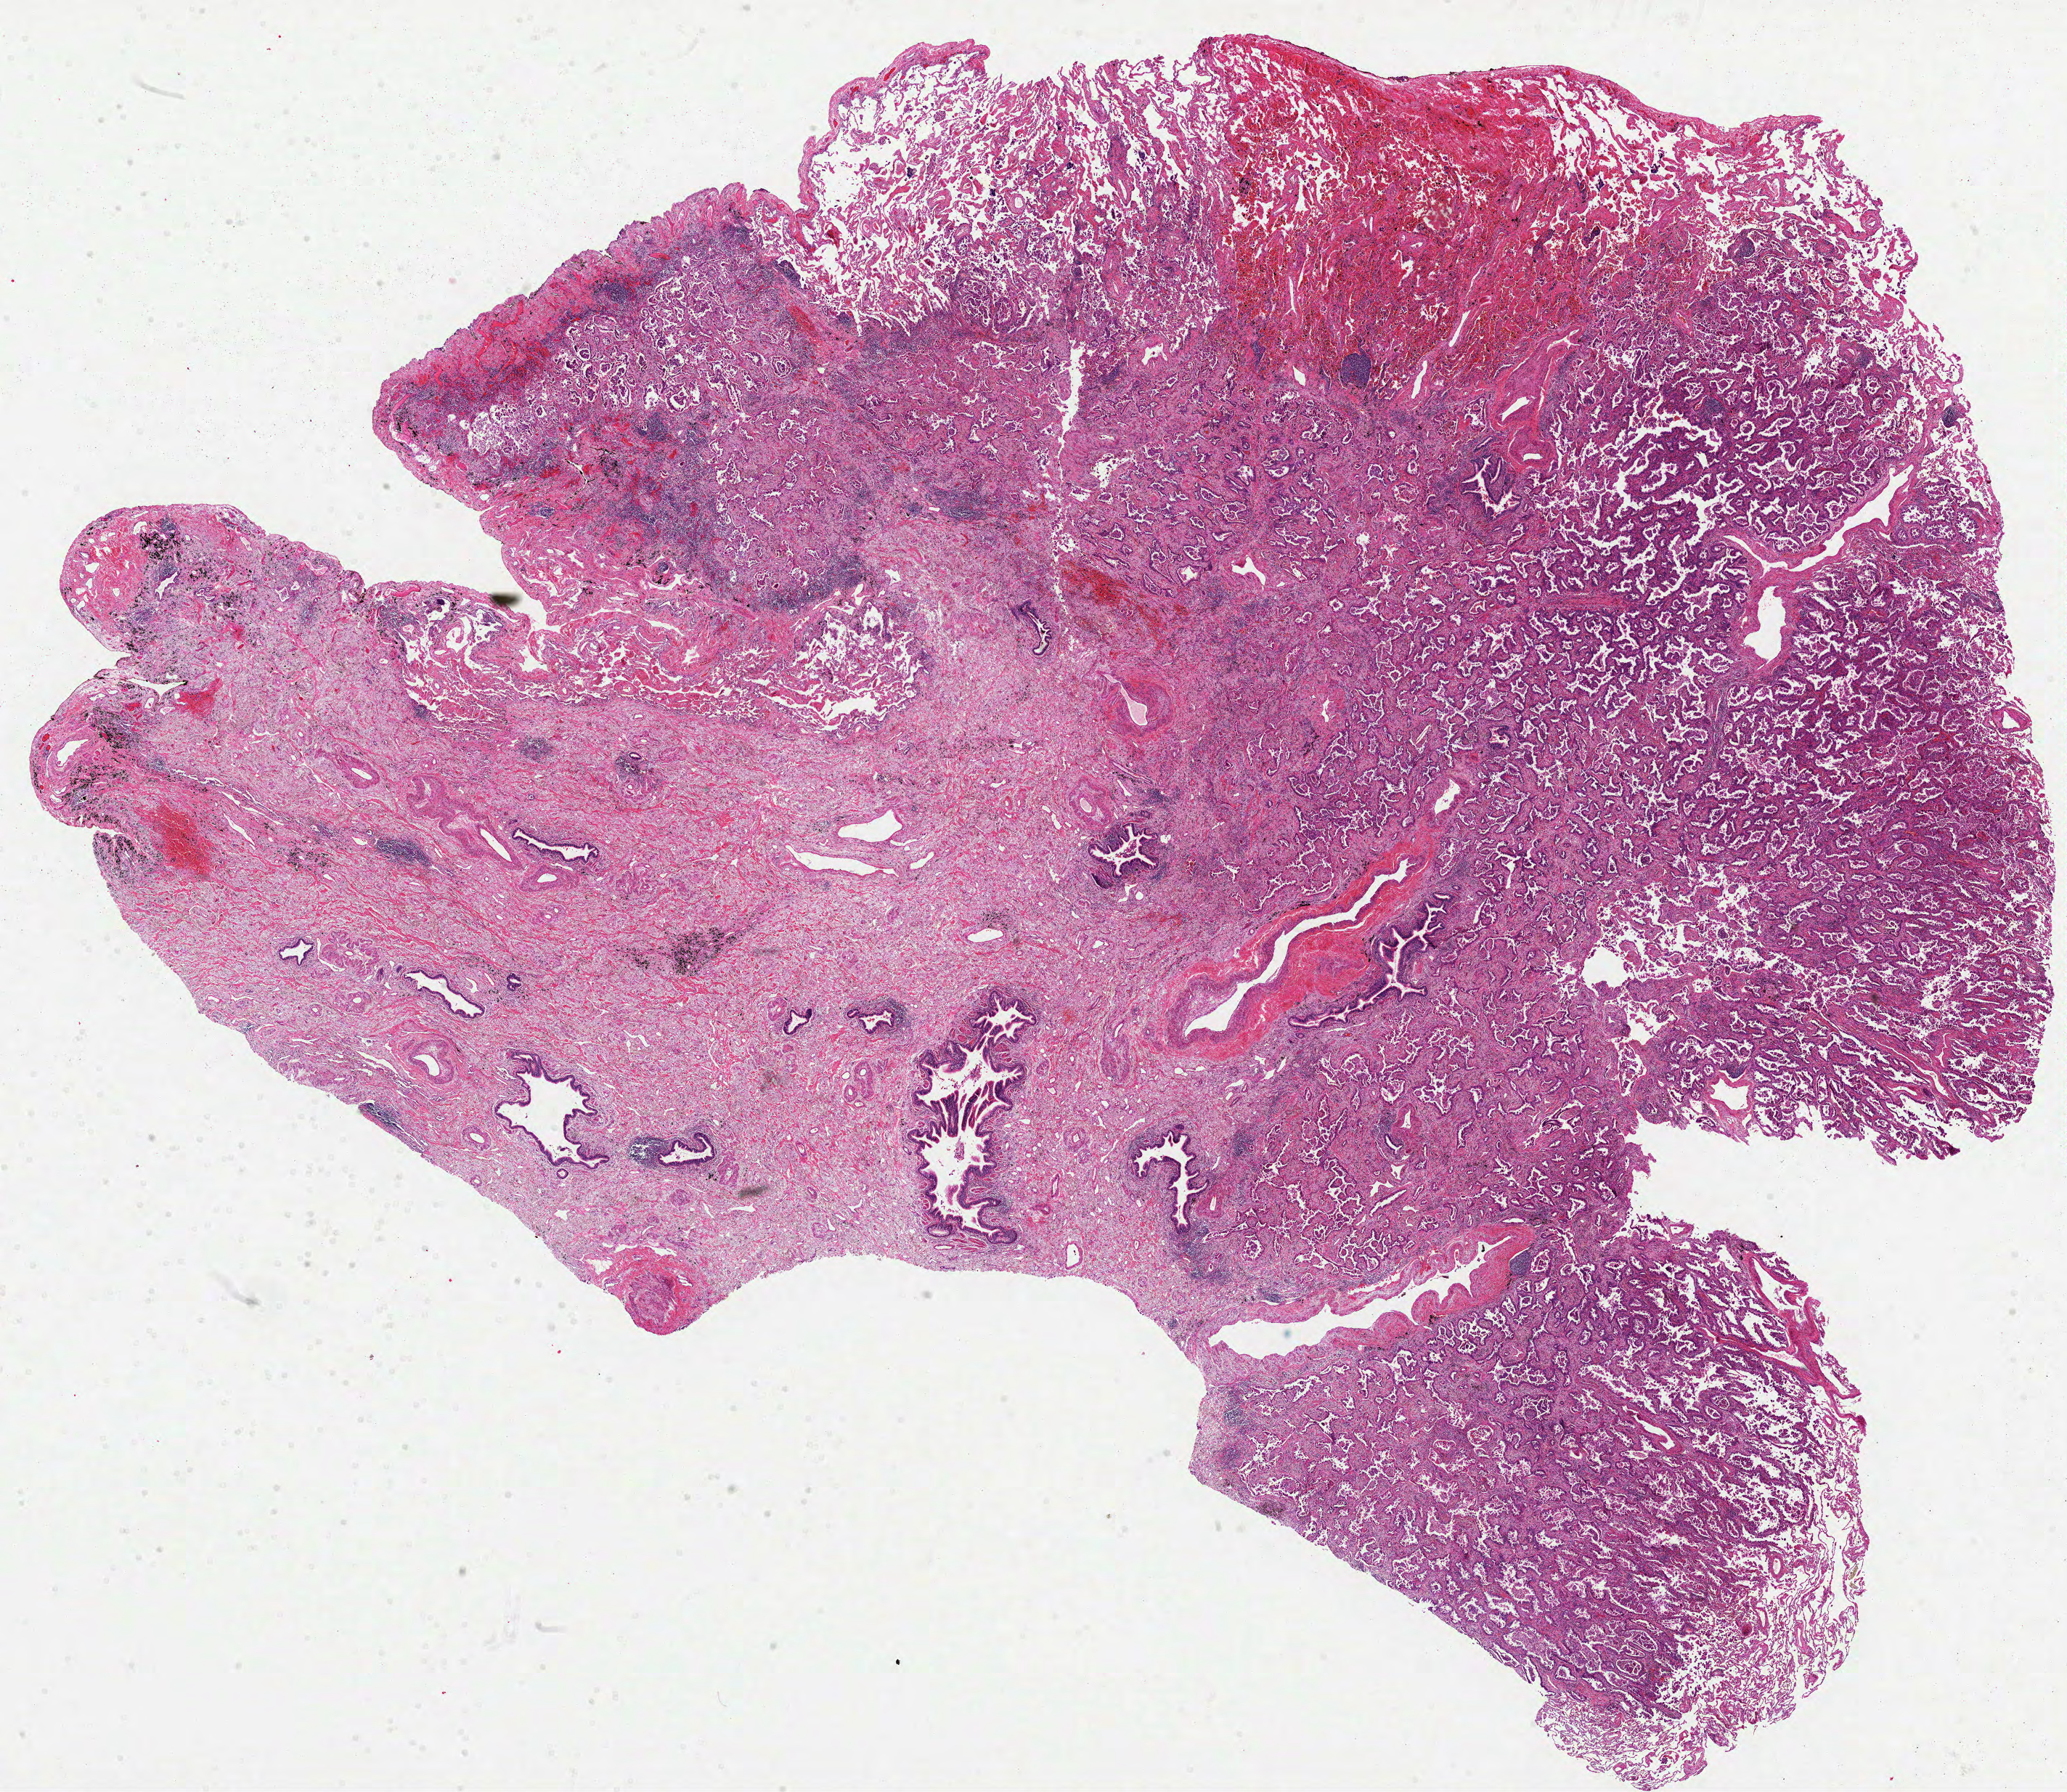
Whole-slide histology image, H&E — whole scanned area (about 23.0 x 19.9 mm, acquisition: 40x scan) shown as a low-resolution overview; FFPE section; lung, primary tumour sample. Female, age 61 years at initial diagnosis.
Diagnosis: Adenocarcinoma, NOS. Laterality: right. AJCC pathologic stage: IIB.